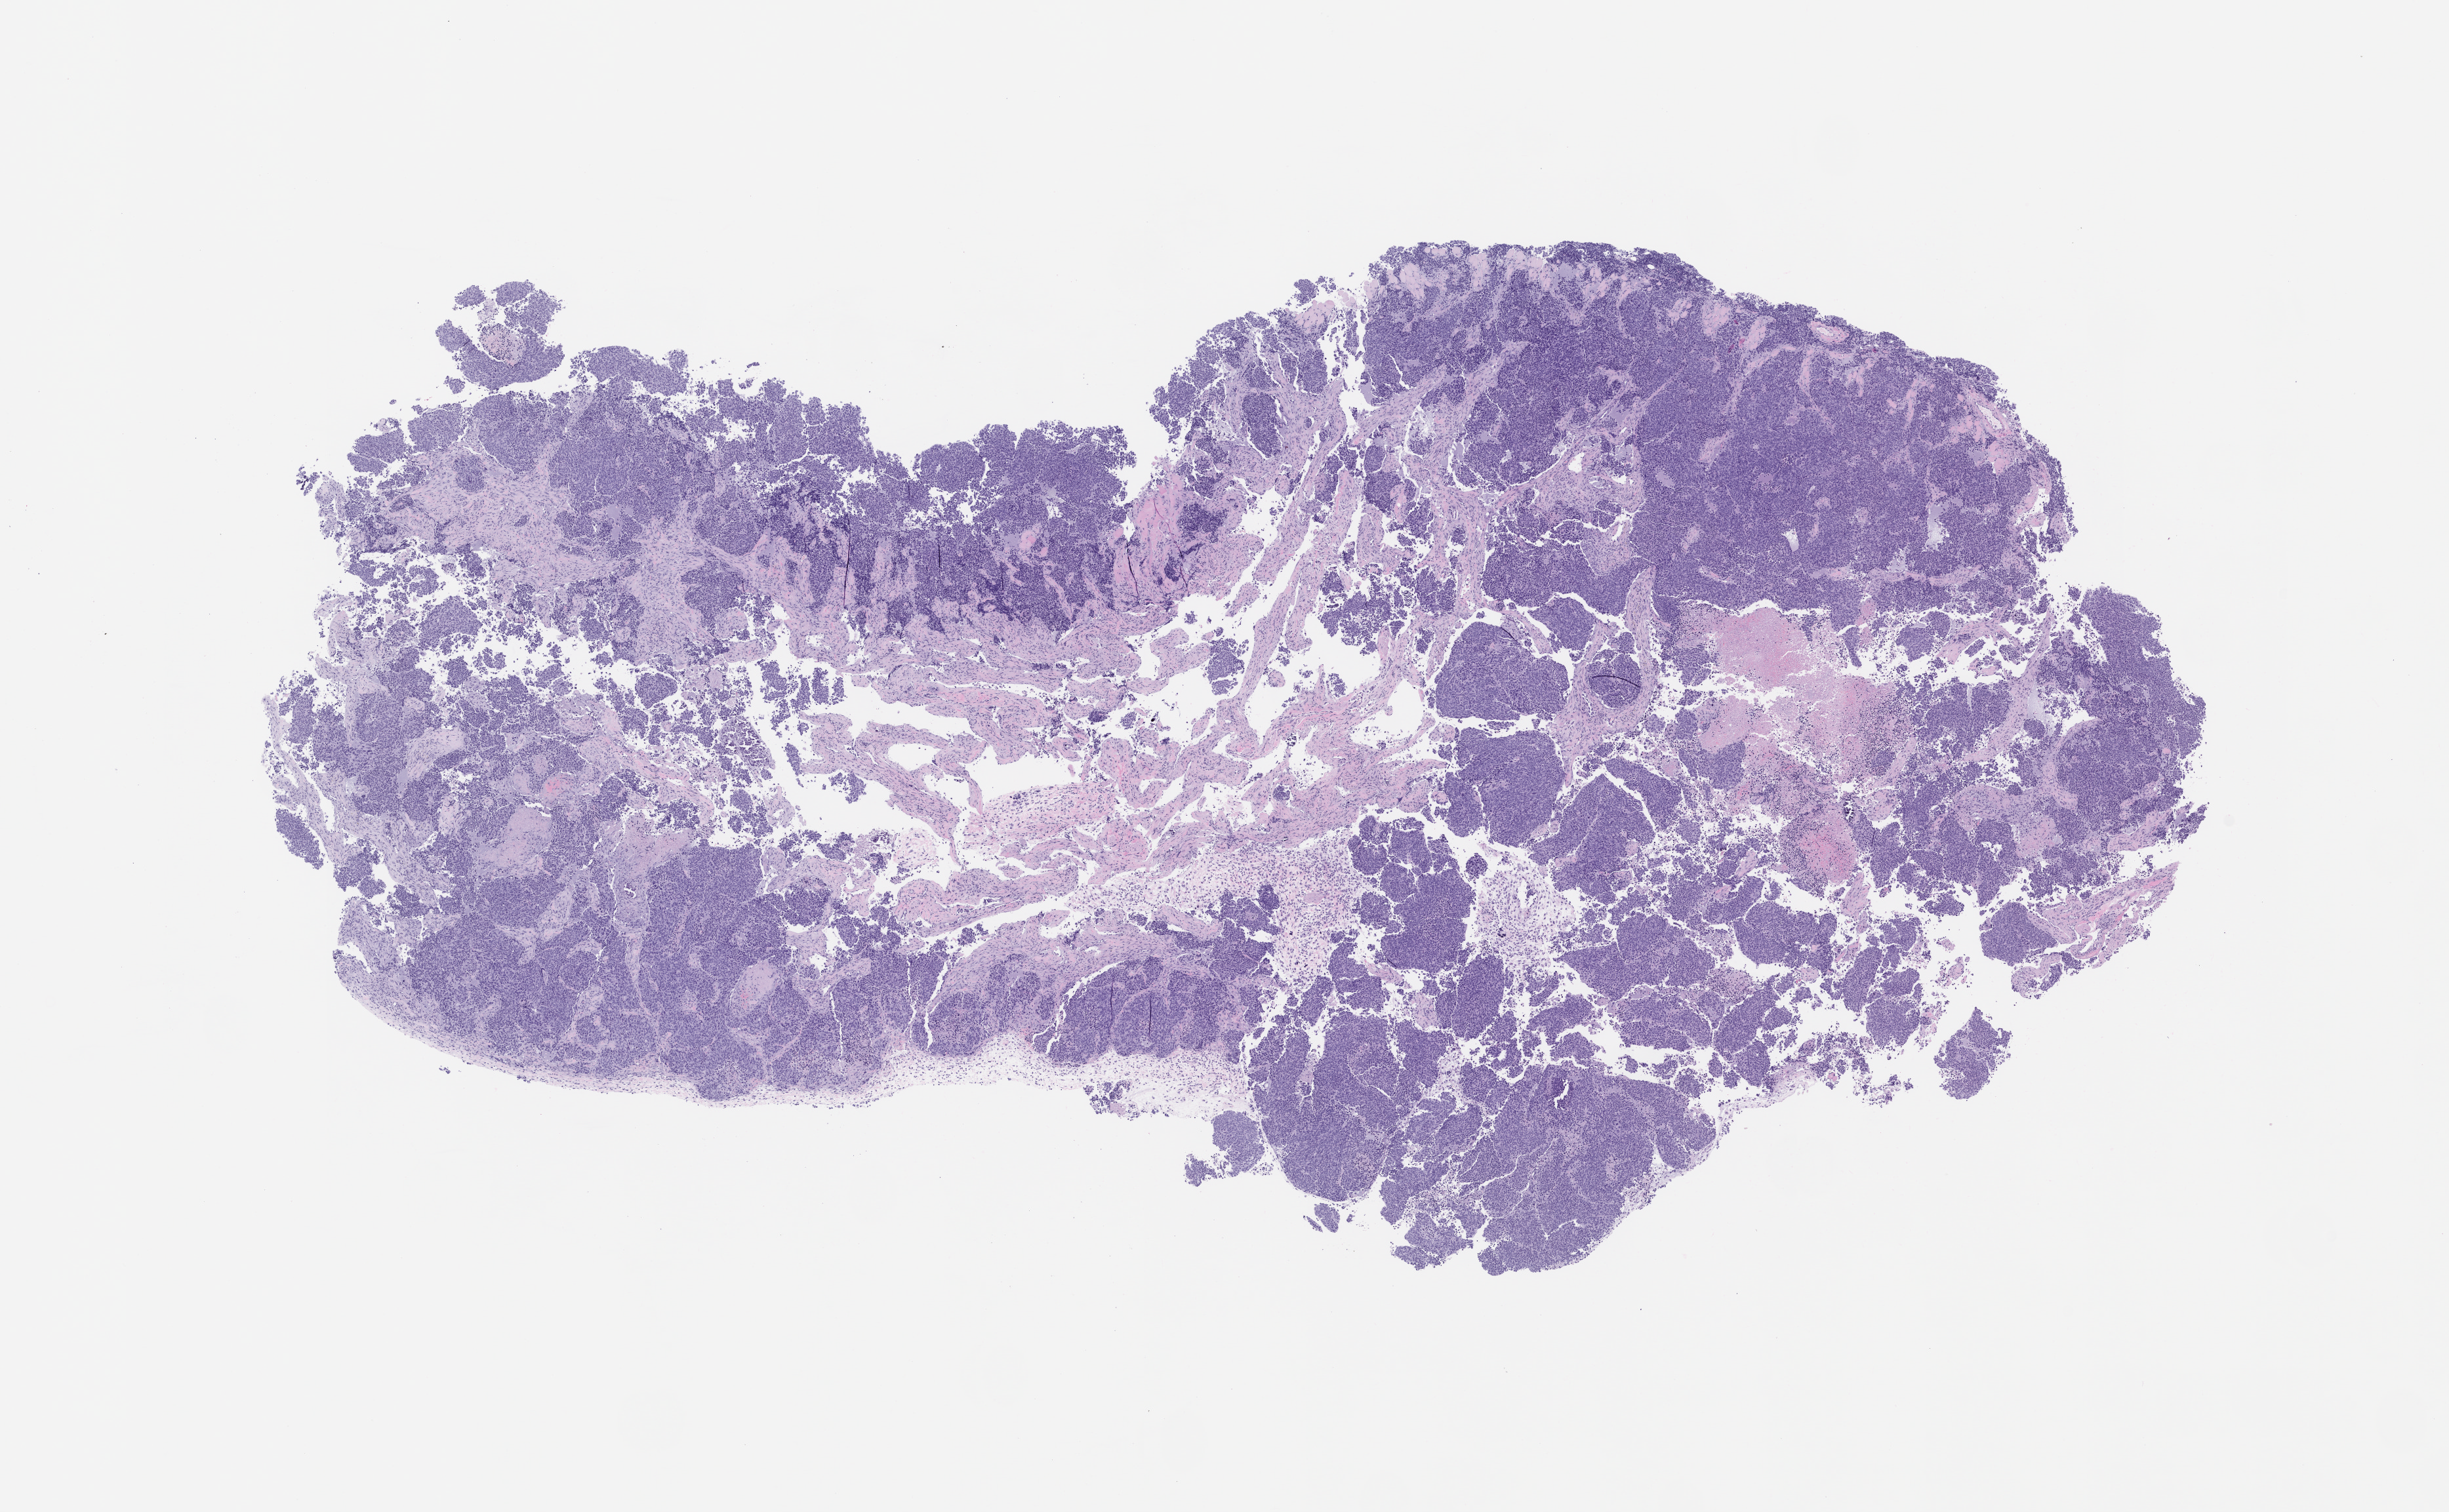
H&E whole-slide image of a patient-derived xenograft (PDX) tumor grown in a mouse — shown as a low-resolution overview of the whole scanned area (about 15.0 x 9.2 mm), formalin-fixed paraffin-embedded section, tumor site category: lung.
Originating patient diagnosis: Lung Adenocarcinoma.